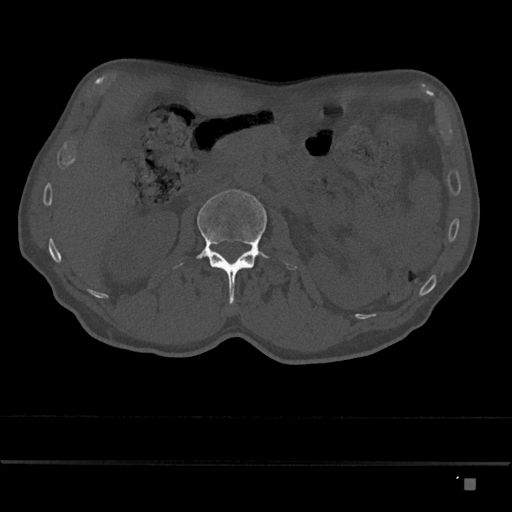
CT including the spine, one axial slice; slice 475 of 797 in the series (ordered by position); reconstruction kernel Br40s/3; bone window (W 1800 / L 400 HU); 512 × 512 image matrix, field of view 390 × 390 mm. Patient: male, 72 years. From the clinical record (not read from this slice): primary cancer: prostate.
Annotated regions visible in this slice (semi-automatic segmentation, software-assisted and operator-edited):
- L2 vertebra: bounding box (x1, y1, x2, y2) in pixels: (174, 189, 297, 304)